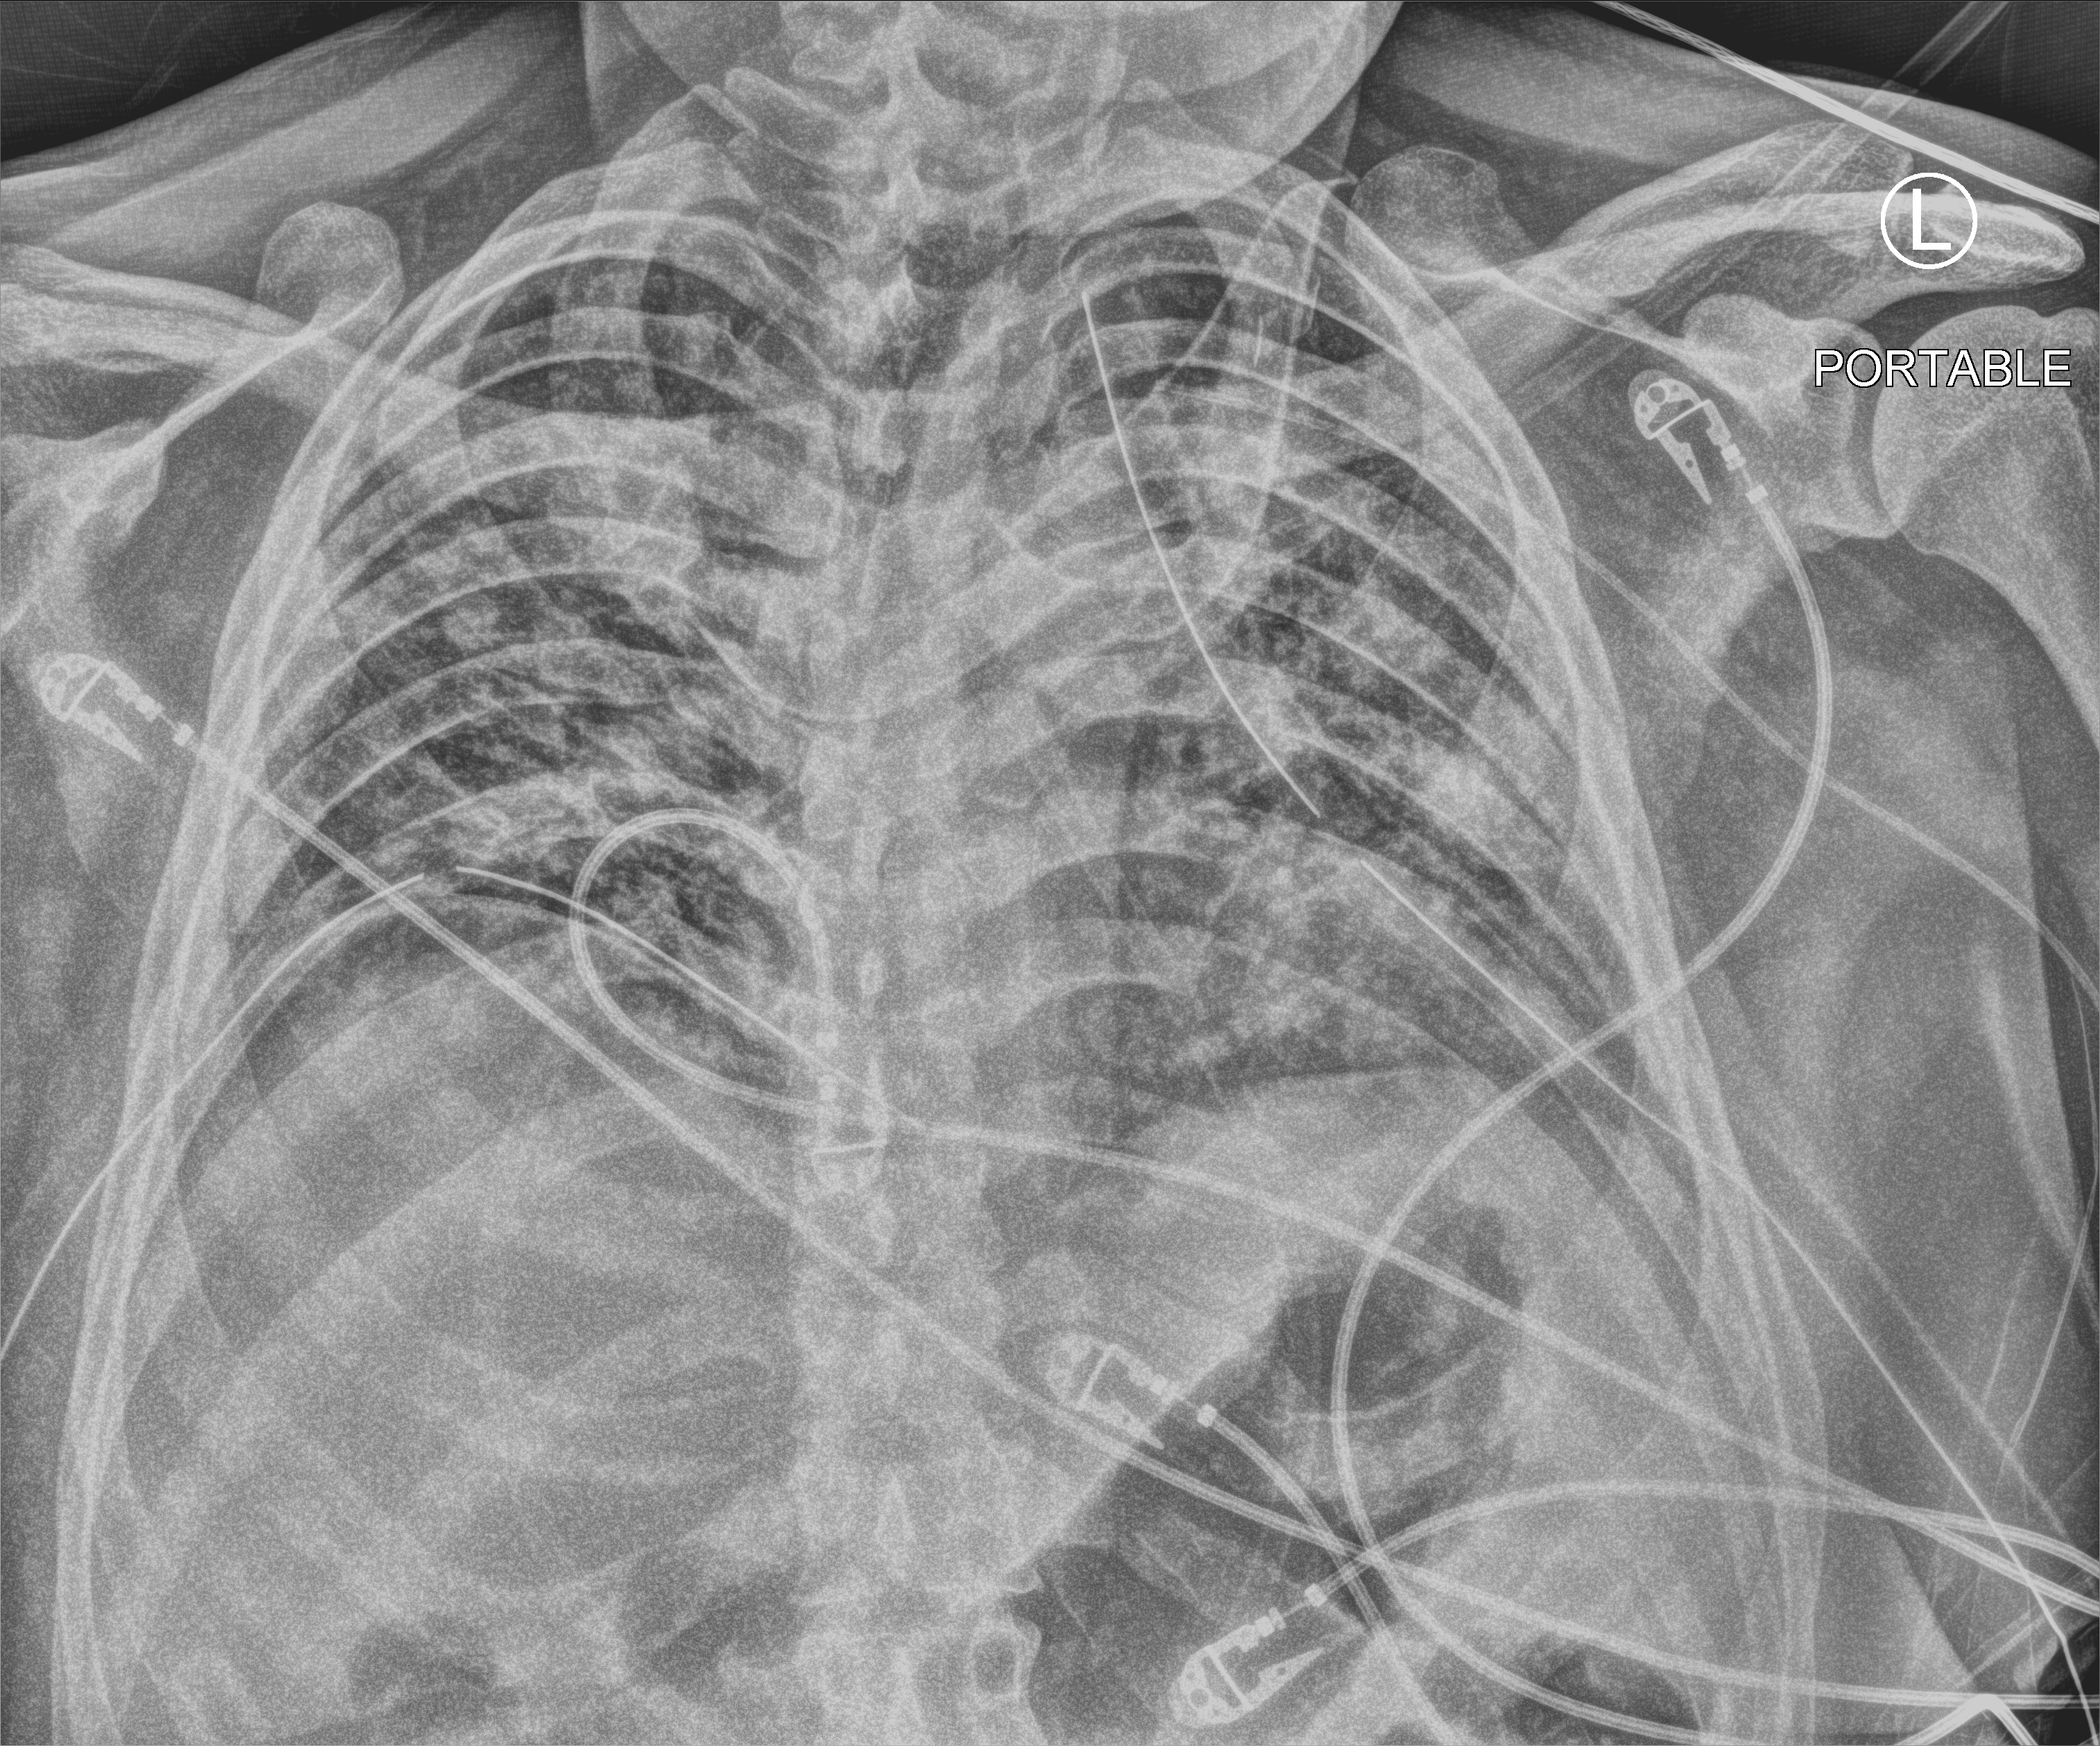
Portable chest radiograph; anteroposterior (AP) projection. Male patient hospitalised with COVID-19, age 18–59 years.
Admission-level facts for this patient (not findings on this image; timing relative to this image not recorded):
- mechanically ventilated during this hospital stay: yes
- length of hospital stay: 29 days